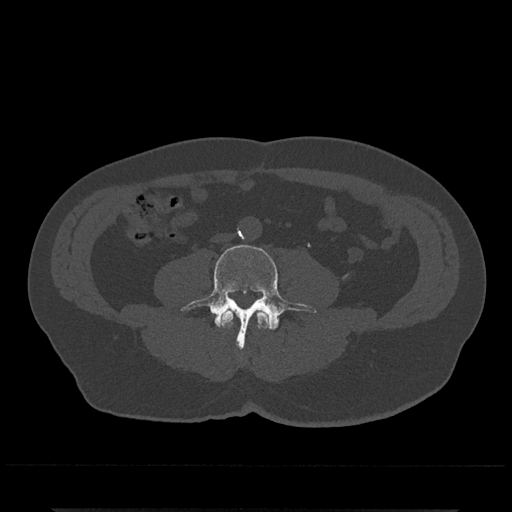
CT including the spine, one axial slice; slice 163 of 797 in the series (ordered by position); 120 kVp; bone window (W 1800 / L 400 HU); 0.5 mm slice thickness; 512 × 512 image matrix. Male patient, age 67 years. Case-level facts recorded for this patient, not image findings: primary cancer: prostate.
Structures marked on this image (semi-automatic segmentation, software-assisted and operator-edited):
- L3 vertebra: box from (x=220, y=310) to (x=270, y=328) px
- L4 vertebra: (x=180, y=244)–(x=317, y=350)